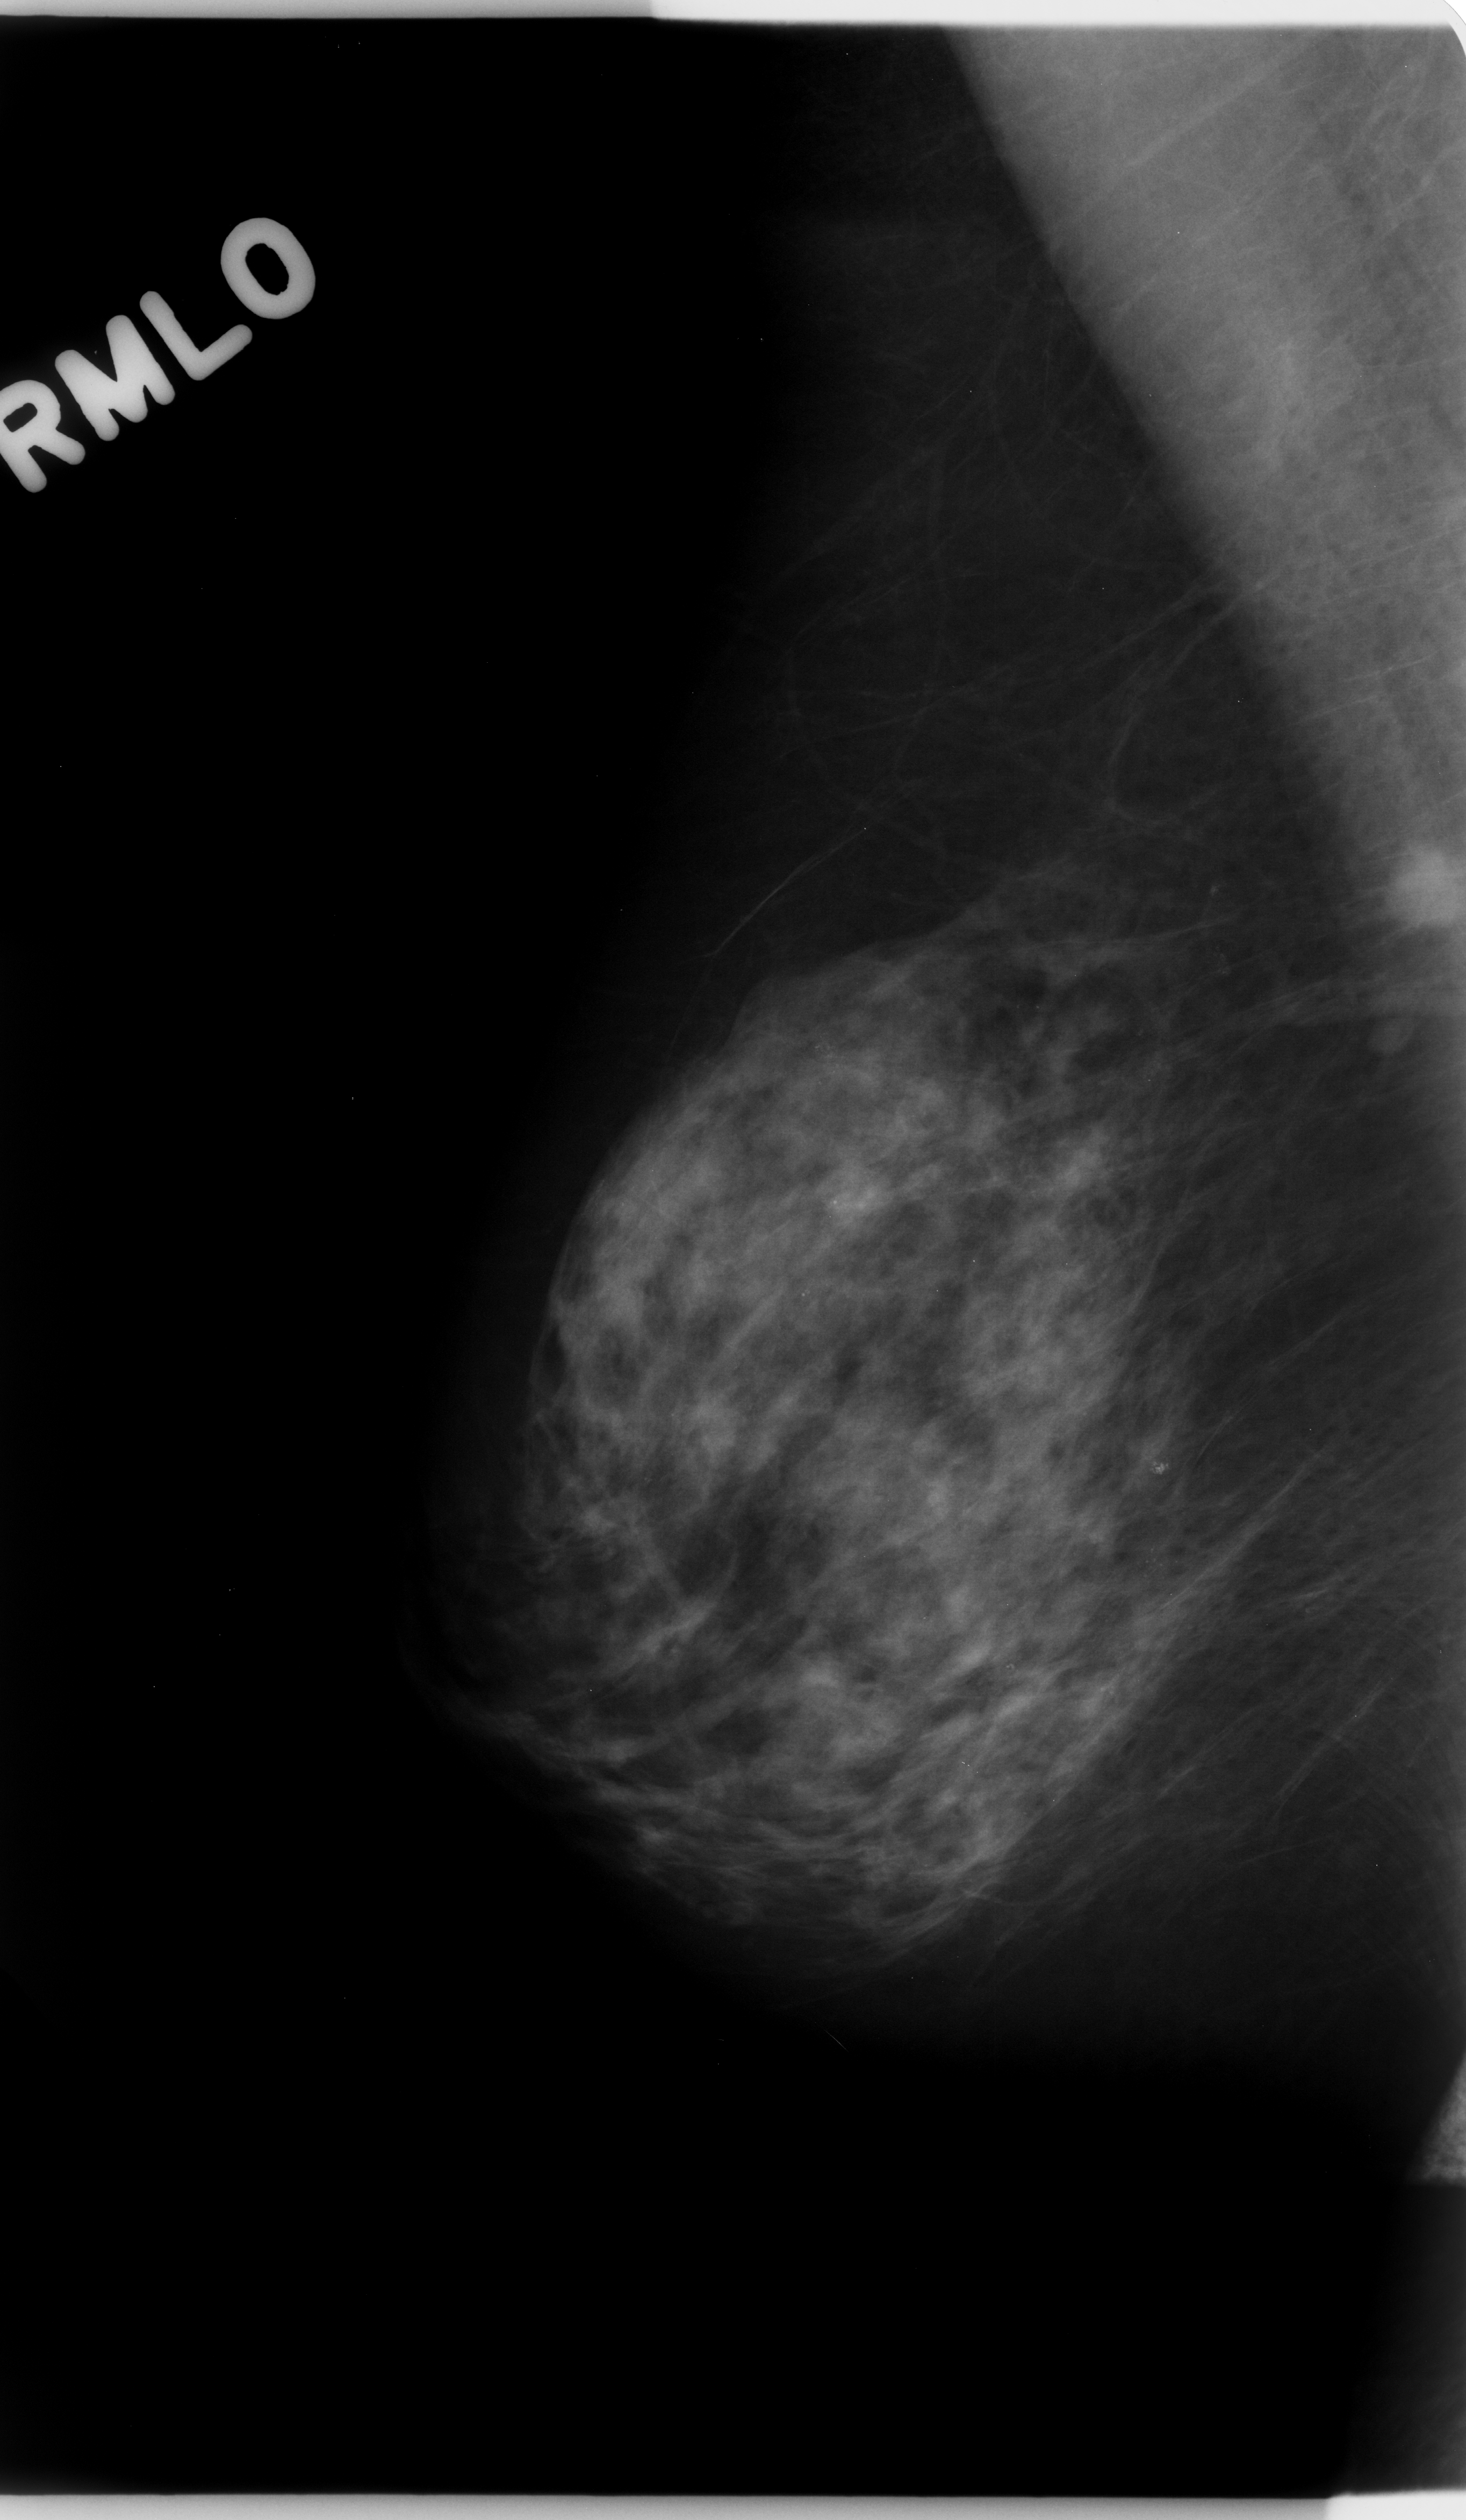
Mammogram (digitized film), right breast, mediolateral oblique (MLO) view, breast composition: scattered fibroglandular densities (BI-RADS density category 2 of 4).
Marked abnormality: mass, shape round, margins microlobulated; BI-RADS assessment category 5; subtlety rating 5 on a 1 (subtle) to 5 (obvious) scale; pathology result (as recorded, not read from the image): malignant.